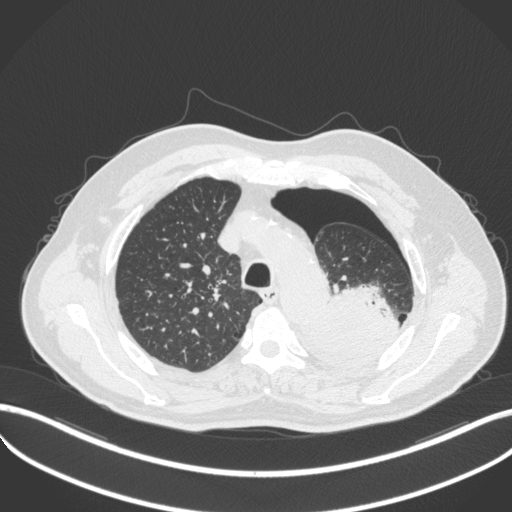
Chest CT, one axial slice. Slice 388 of 466 in the series (ordered by position). Reconstruction kernel B31f. Lung window (W 1500 / L -600 HU). 512 × 512 image matrix, field of view 400 × 400 mm. Patient: male, 76 years. From the clinical record (not read from this slice): clinical TNM (as recorded): T3 N0 M1b.
Structures marked on this image (rectangle marked by the reading radiologist):
- lung tumour (recorded histology: adenocarcinoma): bounding box [x1, y1, x2, y2] px = [298, 285, 391, 378]